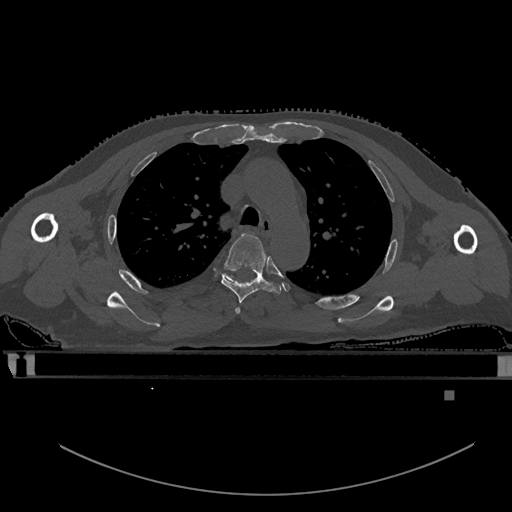
CT including the spine, one axial slice; position 404 of 969 along the scan axis; bone window (W 1800 / L 400 HU); 512 × 512 image matrix, field of view 456 × 456 mm. Male patient, age 82 years. From the clinical record (not read from this slice): primary cancer: prostate; vertebrae with lytic lesions (as recorded): T11, T9, T8, T2.
Outlined on this slice (semi-automatically segmented with operator editing):
- T3 vertebra: bounding box <235,307,241,314> (left, top, right, bottom; pixels)
- T4 vertebra: <221,233,281,304>
- T5 vertebra: <219,273,237,282>